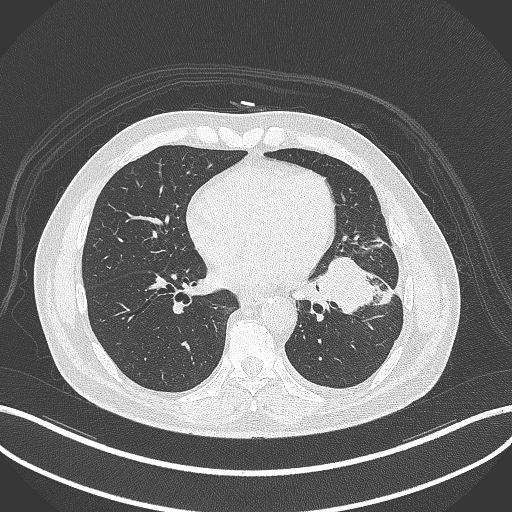
Chest CT, one axial slice; position 147 of 230 along the scan axis; reconstruction kernel B70f; 120 kVp; lung window (W 1500 / L -600 HU); 1 mm slice thickness; 512 × 512 image matrix. Patient: male, 68 years. Case-level facts recorded for this patient, not image findings: clinical TNM (as recorded): T2b N0 M0.
Annotated regions visible in this slice (bounding box drawn by a radiologist):
- lung tumour (recorded histology: squamous cell carcinoma): bounding box <313,251,379,316> (left, top, right, bottom; pixels)